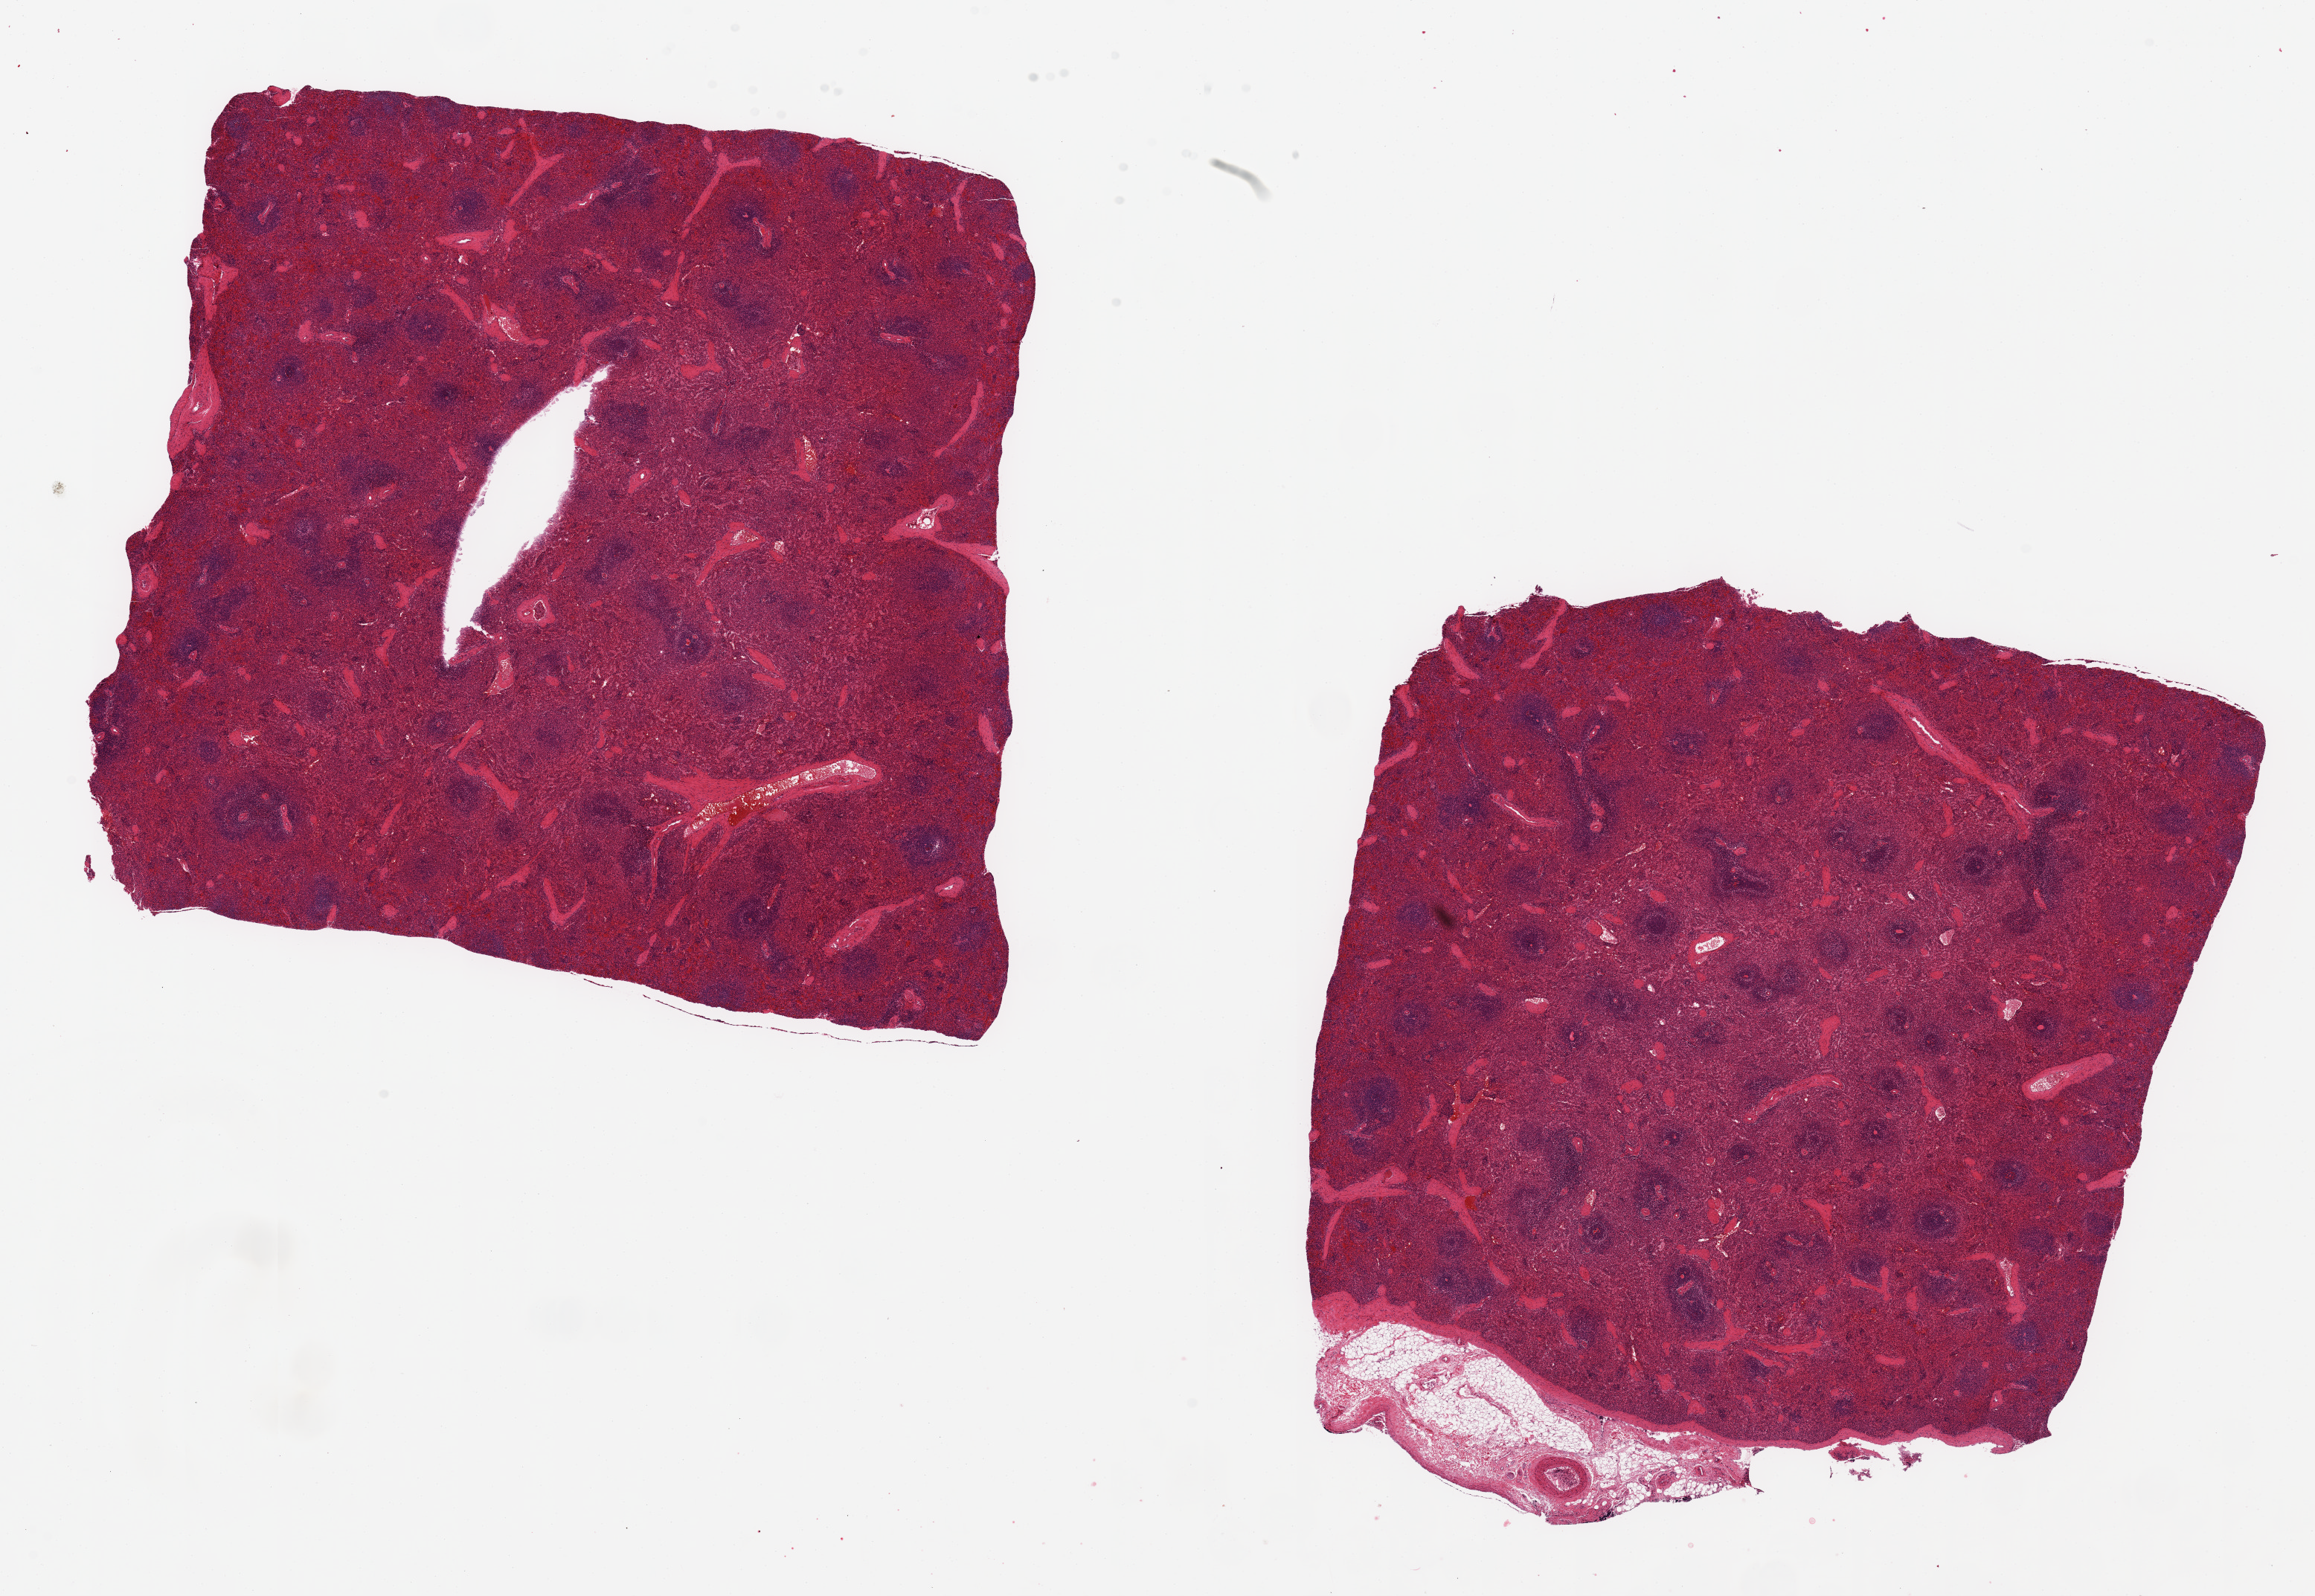
Whole-slide image, haematoxylin and eosin stain, brightfield — a low-resolution overview of the entire scanned area, about 24.6 x 17.0 mm (acquisition: 20x scan); PAXgene-fixed paraffin-embedded (PFPE) section; target tissue: spleen; tissue donor sample. Donor: female.
Review note (as recorded): 2, 9mm cubes, slightly congested.